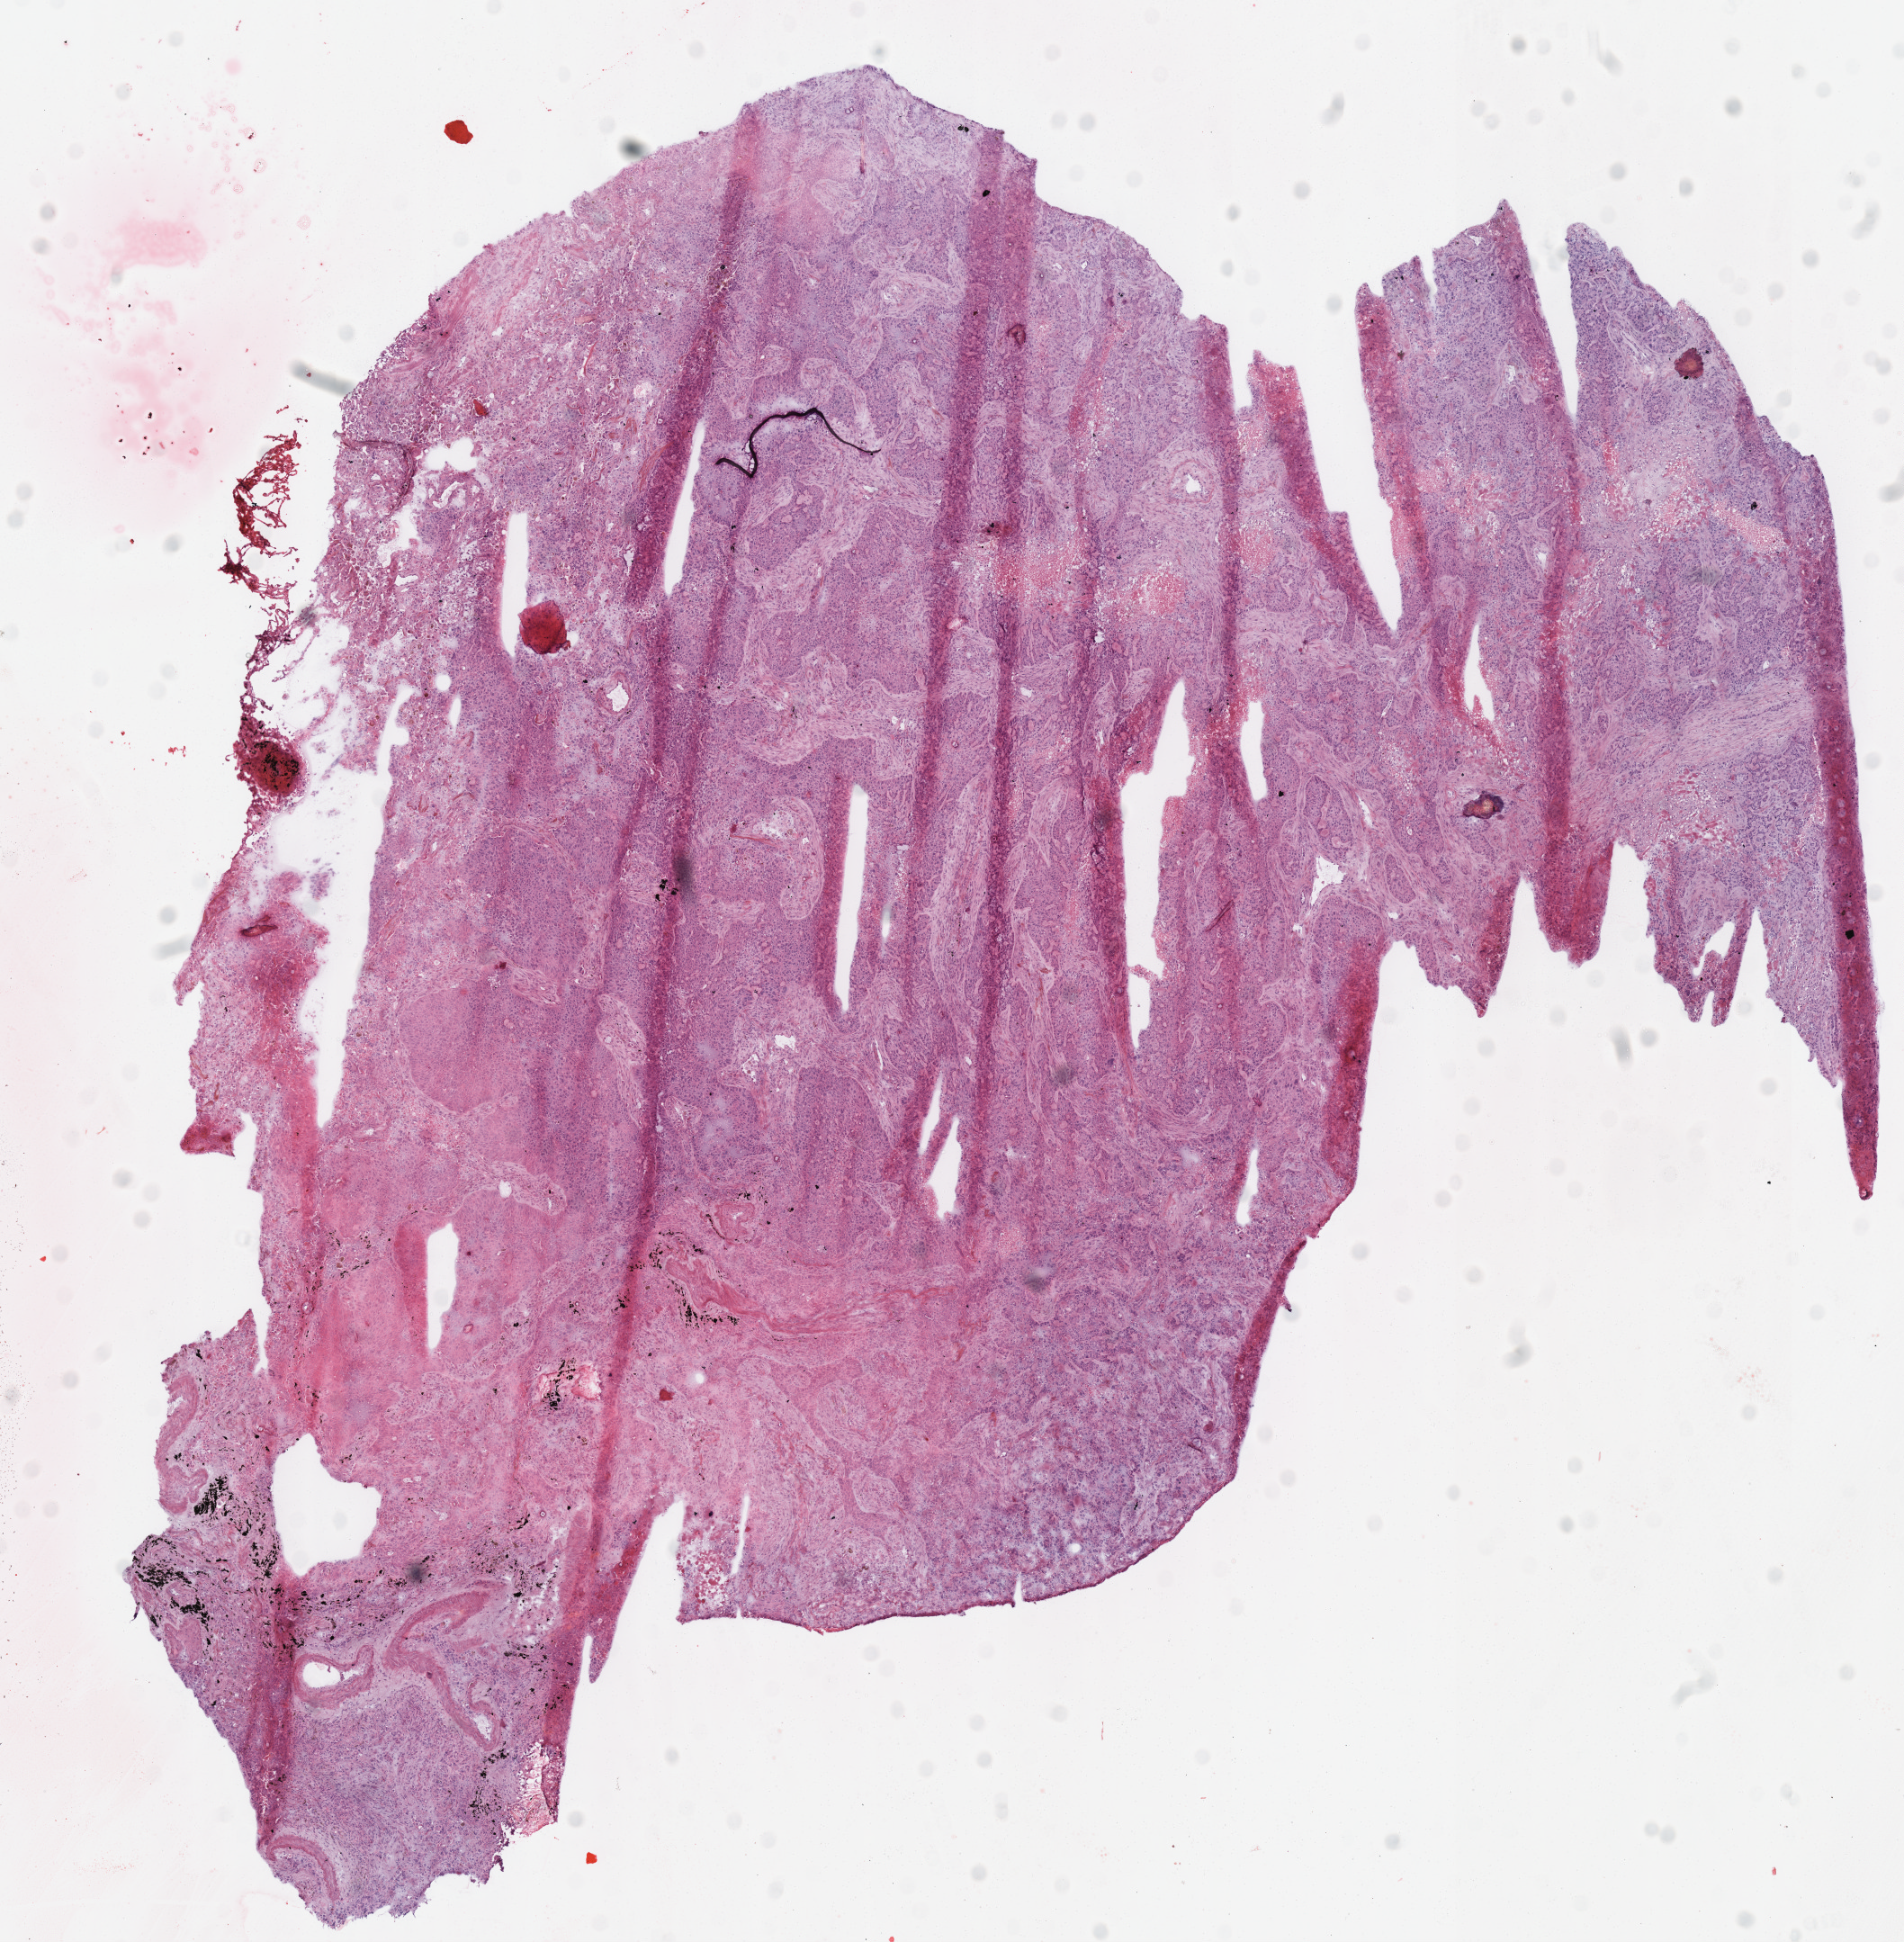
Whole-slide histology image, H&E-stained — a low-resolution overview of the entire scanned area, about 8.3 x 8.5 mm (slide scanned at 40x). Frozen section from the top of the tissue portion. Lung, primary tumour sample. Male, age 60 years at initial diagnosis. Pathologist review of this section (percent, as recorded): tumour cells 65%, tumour nuclei 72%, normal cells 5%, stromal cells 15%, necrosis 15%. Infiltration values recorded for this section: lymphocyte infiltration 3%, monocyte infiltration 2%.
AJCC pathologic stage: IB. Diagnosis: Basaloid squamous cell carcinoma.